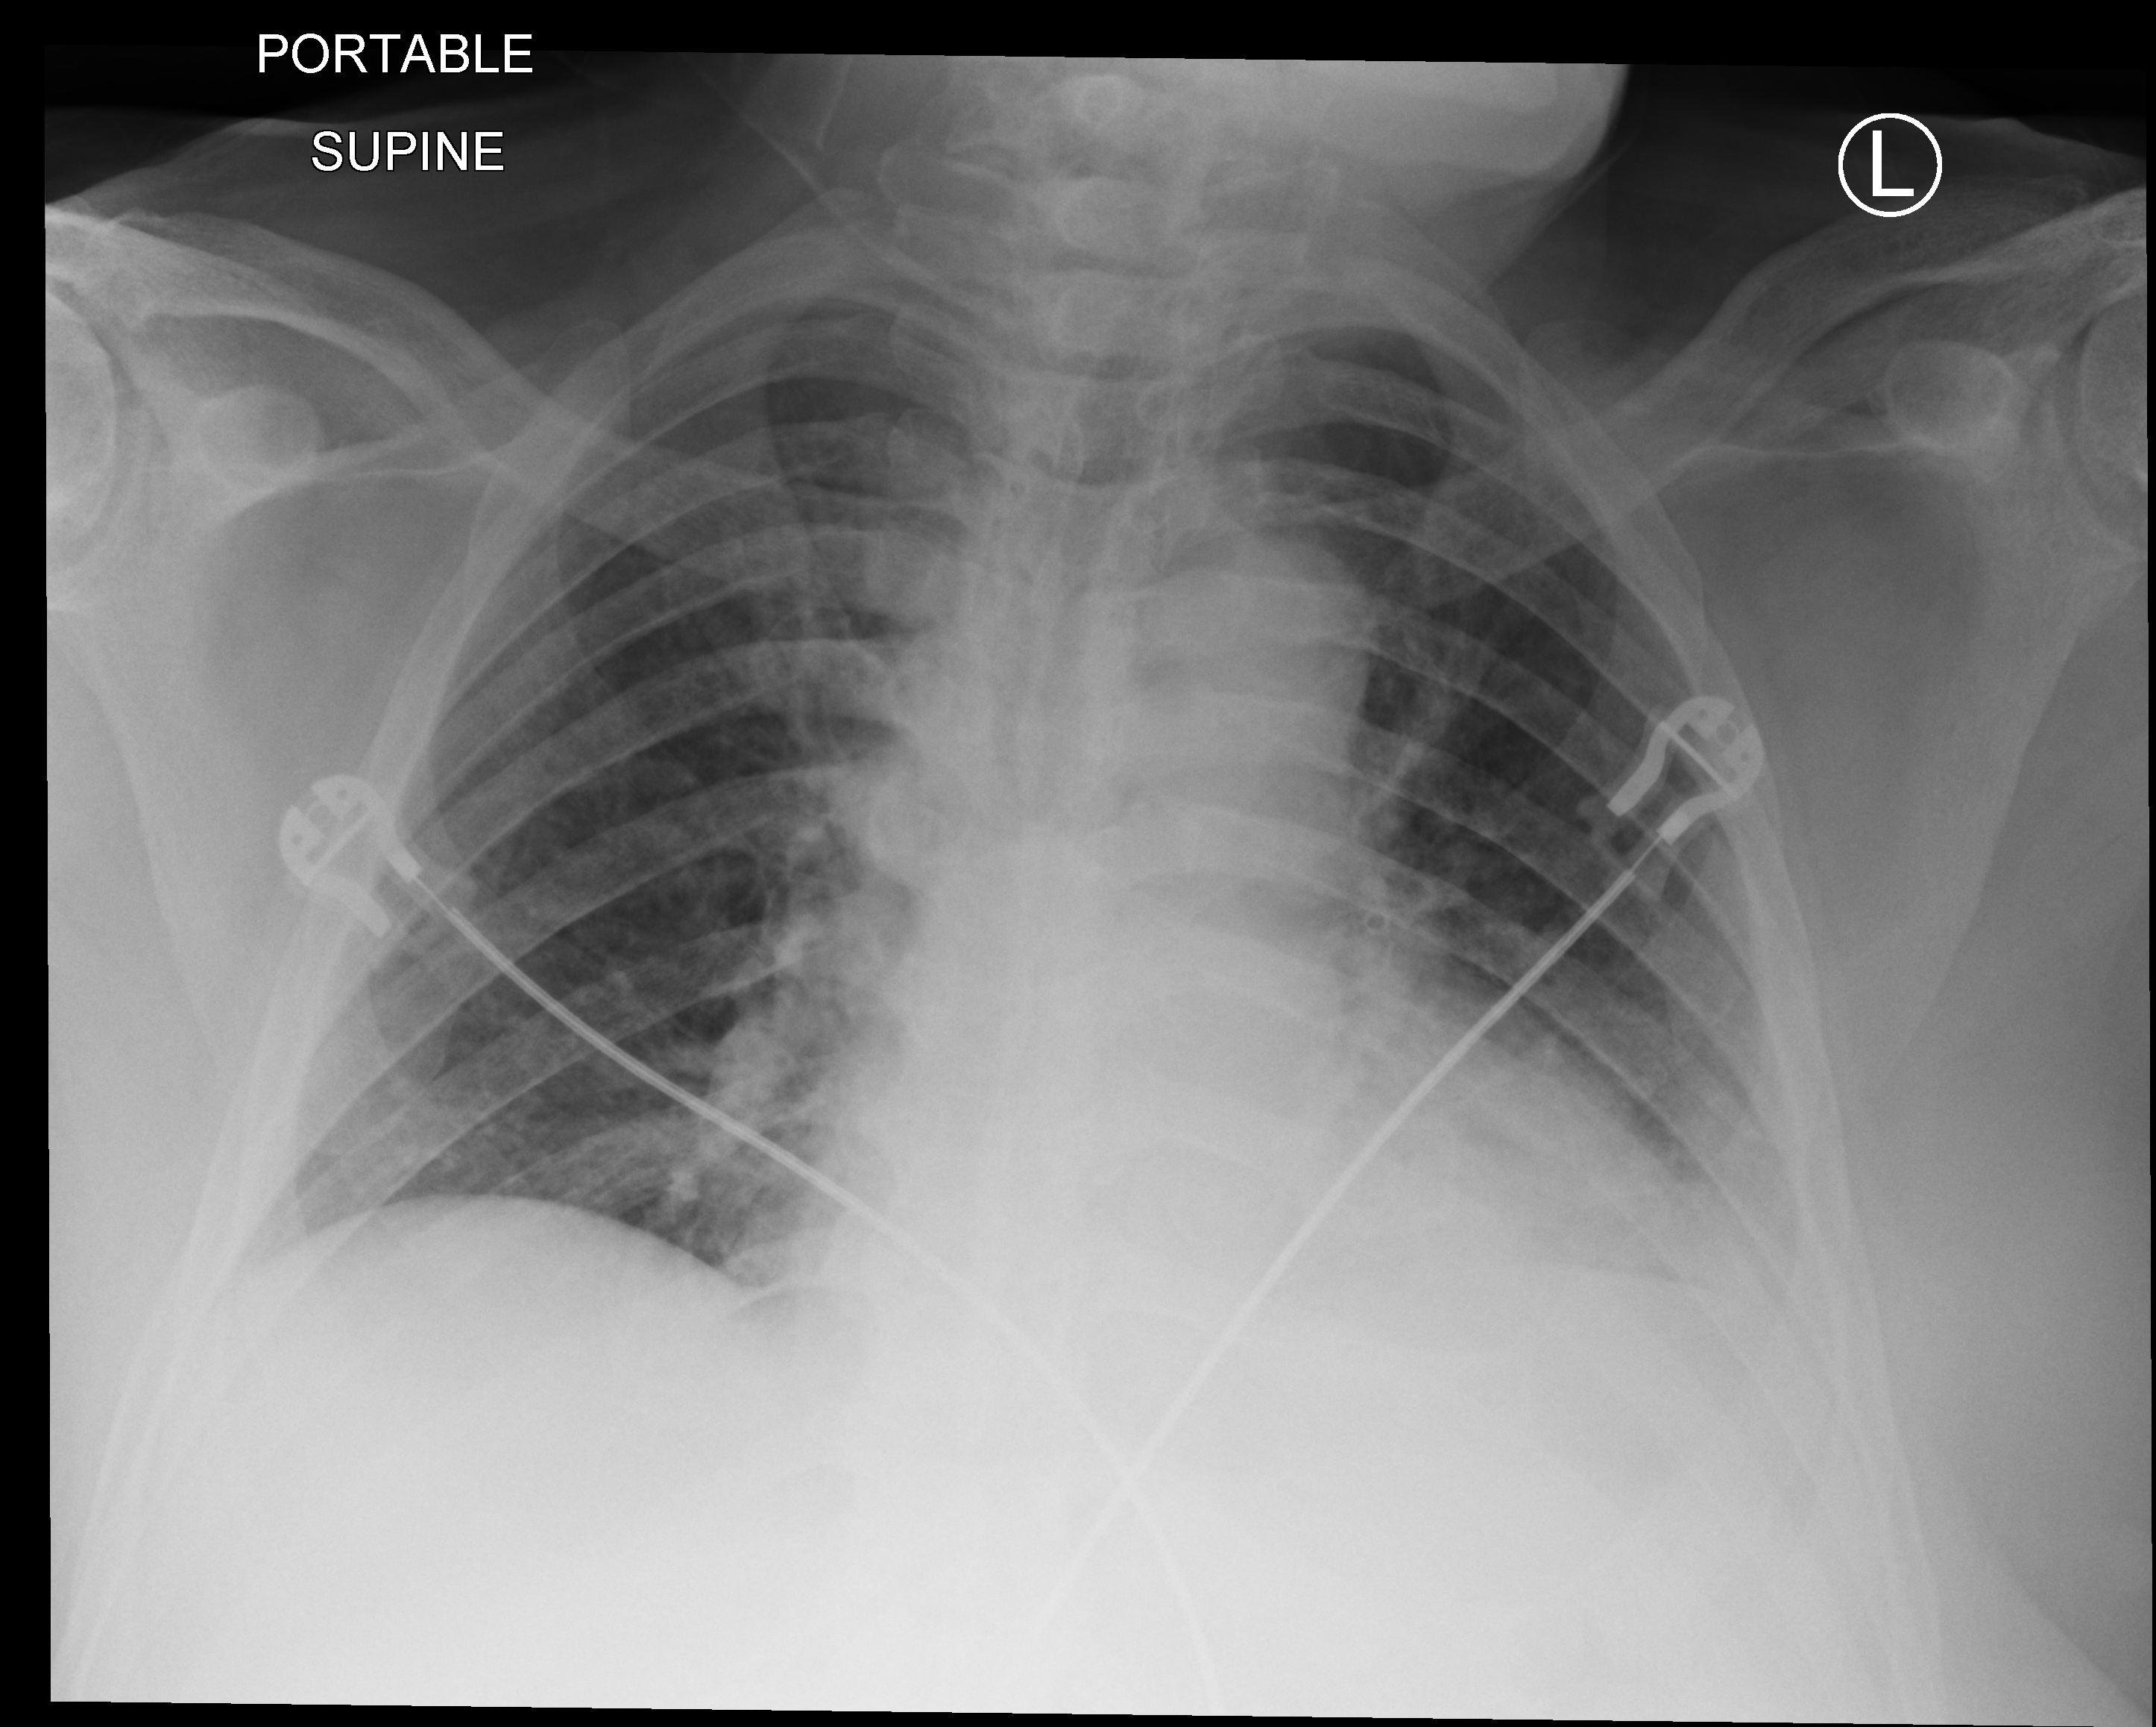
Bedside chest radiograph (computed radiography); anteroposterior (AP) projection. Male patient hospitalised with COVID-19, age 75–90 years.
Hospital-stay facts (about this admission, not read from this image; timing relative to this image not recorded): admitted to intensive care during this hospital stay: yes.